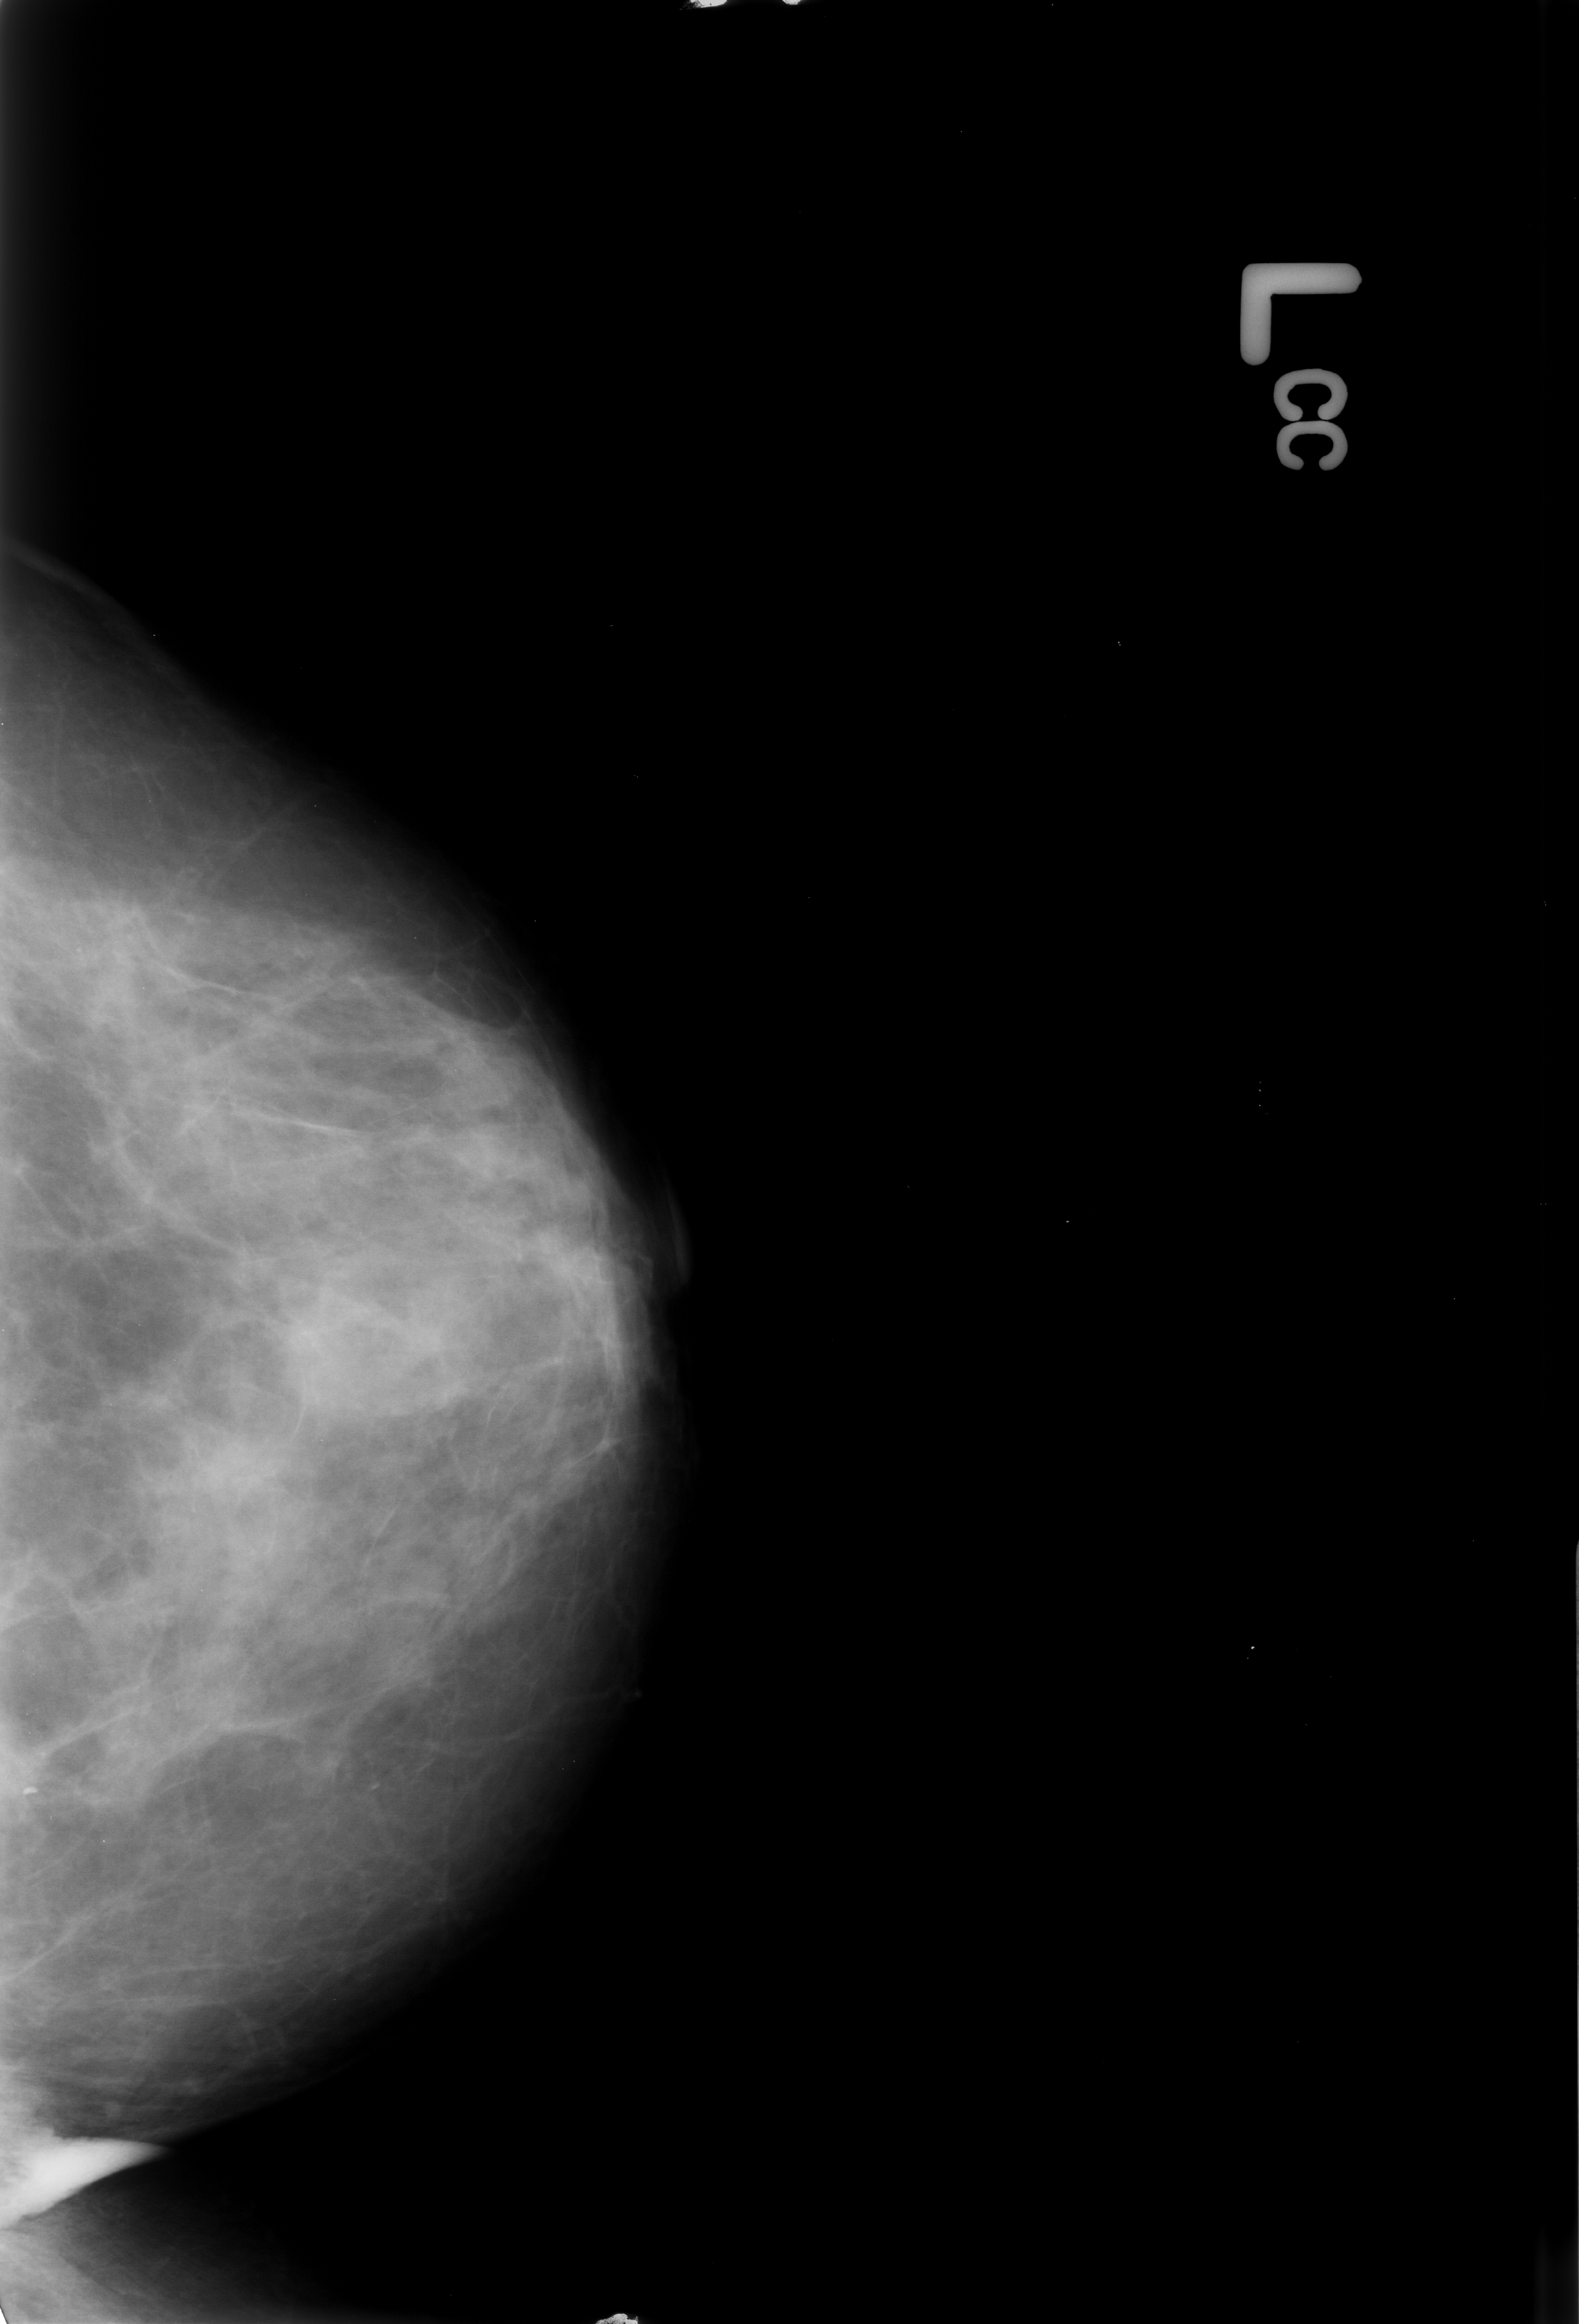
Scanned film-screen mammogram, left breast, craniocaudal (CC) view, BI-RADS breast density category 3 (scale 1–4).
Abnormality record for this image: calcifications, morphology pleomorphic, distribution clustered; BI-RADS assessment category 4; subtlety rating 3 on a 1 (subtle) to 5 (obvious) scale; pathology (as recorded): malignant.